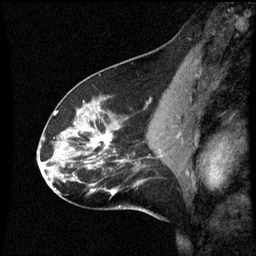
Breast MRI (dynamic contrast-enhanced), one sagittal slice; position 30 of 60 along the scan axis; dynamic contrast-enhanced series, image 2 of 3 at this slice position (ordered by acquisition); 1.5 T; TE 4.2 ms, TR 8.9 ms; 2 mm slice thickness; 256 × 256 image matrix, field of view 200 × 200 mm. Female patient, age 45 years. From the clinical record (not read from this slice): setting: breast cancer imaged before/during neoadjuvant chemotherapy; receptor status: HR-positive, HER2-negative.
Structures marked on this image (semi-automatically segmented with operator editing):
- analysis volume of interest (the breast-tissue region the enhancement analysis was run in; not a lesion): bounding box [x1, y1, x2, y2] px = [46, 94, 171, 205]
- tumour enhancement mask (voxels above the 70 % enhancement threshold inside the analysis volume of interest): [92, 134, 123, 163]